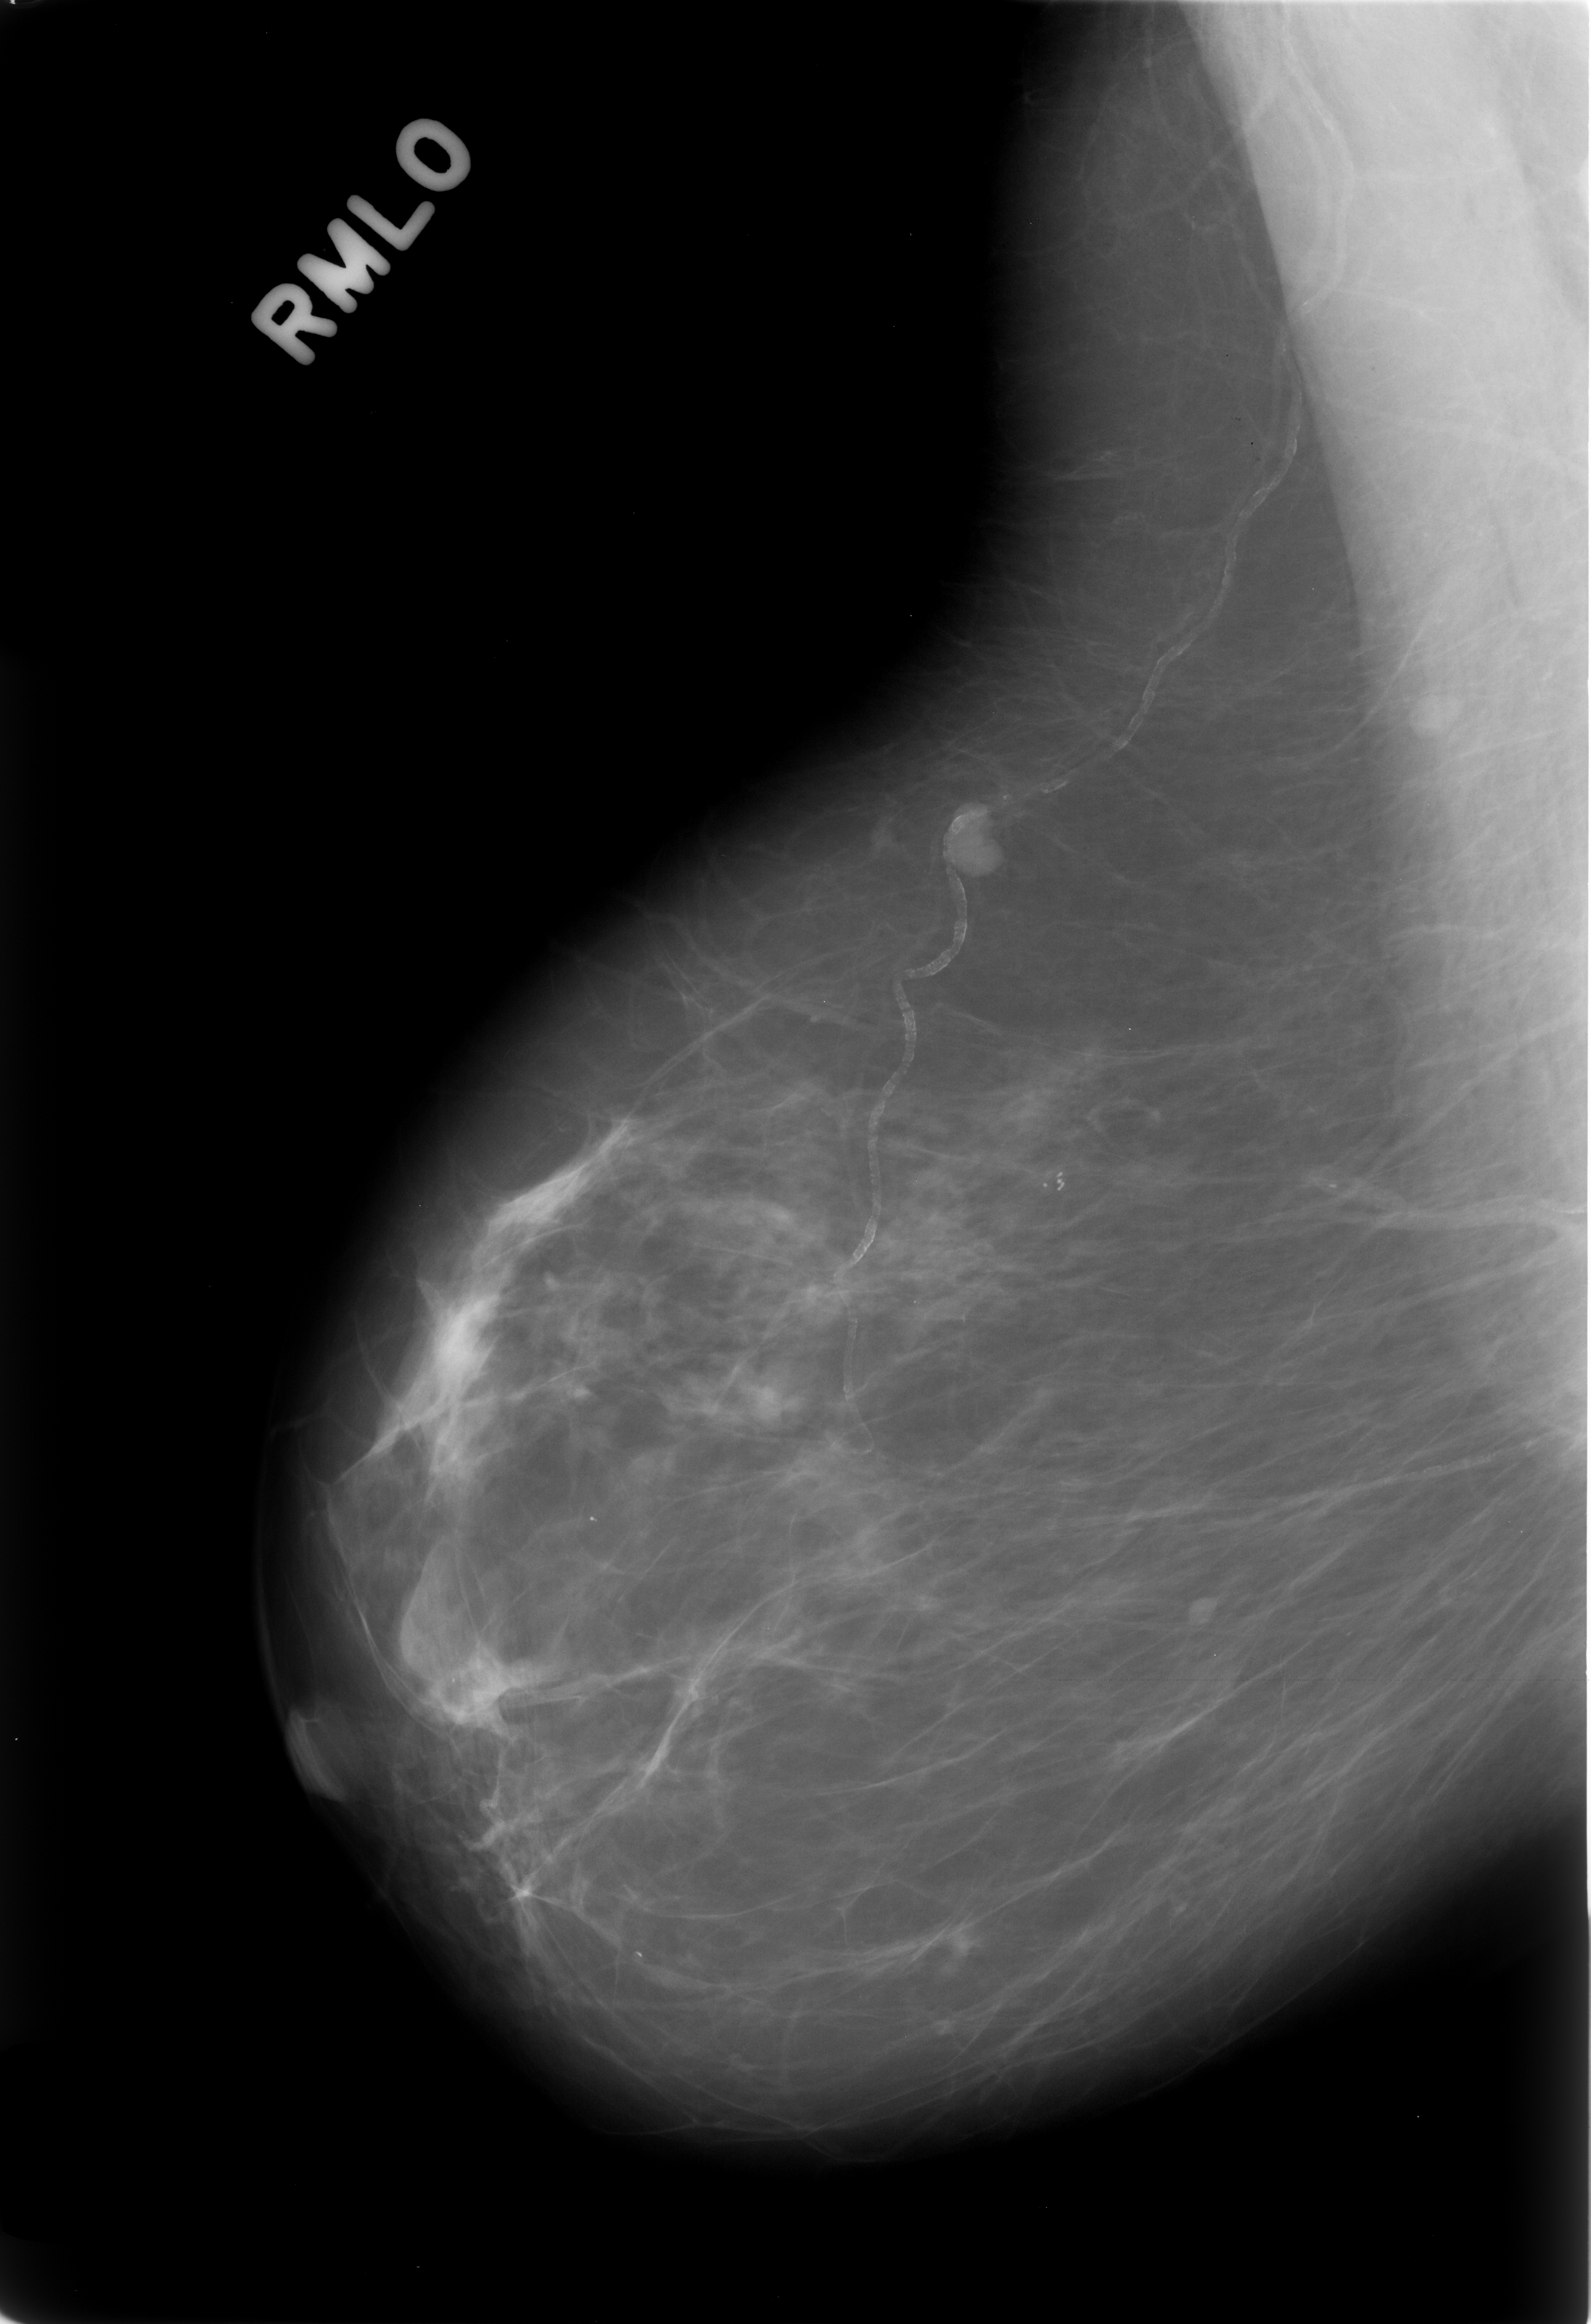
Digitized screen-film mammogram; right breast; mediolateral oblique (MLO) view; BI-RADS breast density category 1 (scale 1–4); 1591 × 2324 image matrix.
Marked abnormalities (boxes around the expert regions of interest):
- mass, shape lobulated, margins circumscribed; BI-RADS assessment category 3; subtlety rating 5 on a 1 (subtle) to 5 (obvious) scale; pathology (as recorded): benign: bounding box [x1, y1, x2, y2] px = [936, 797, 1008, 879]